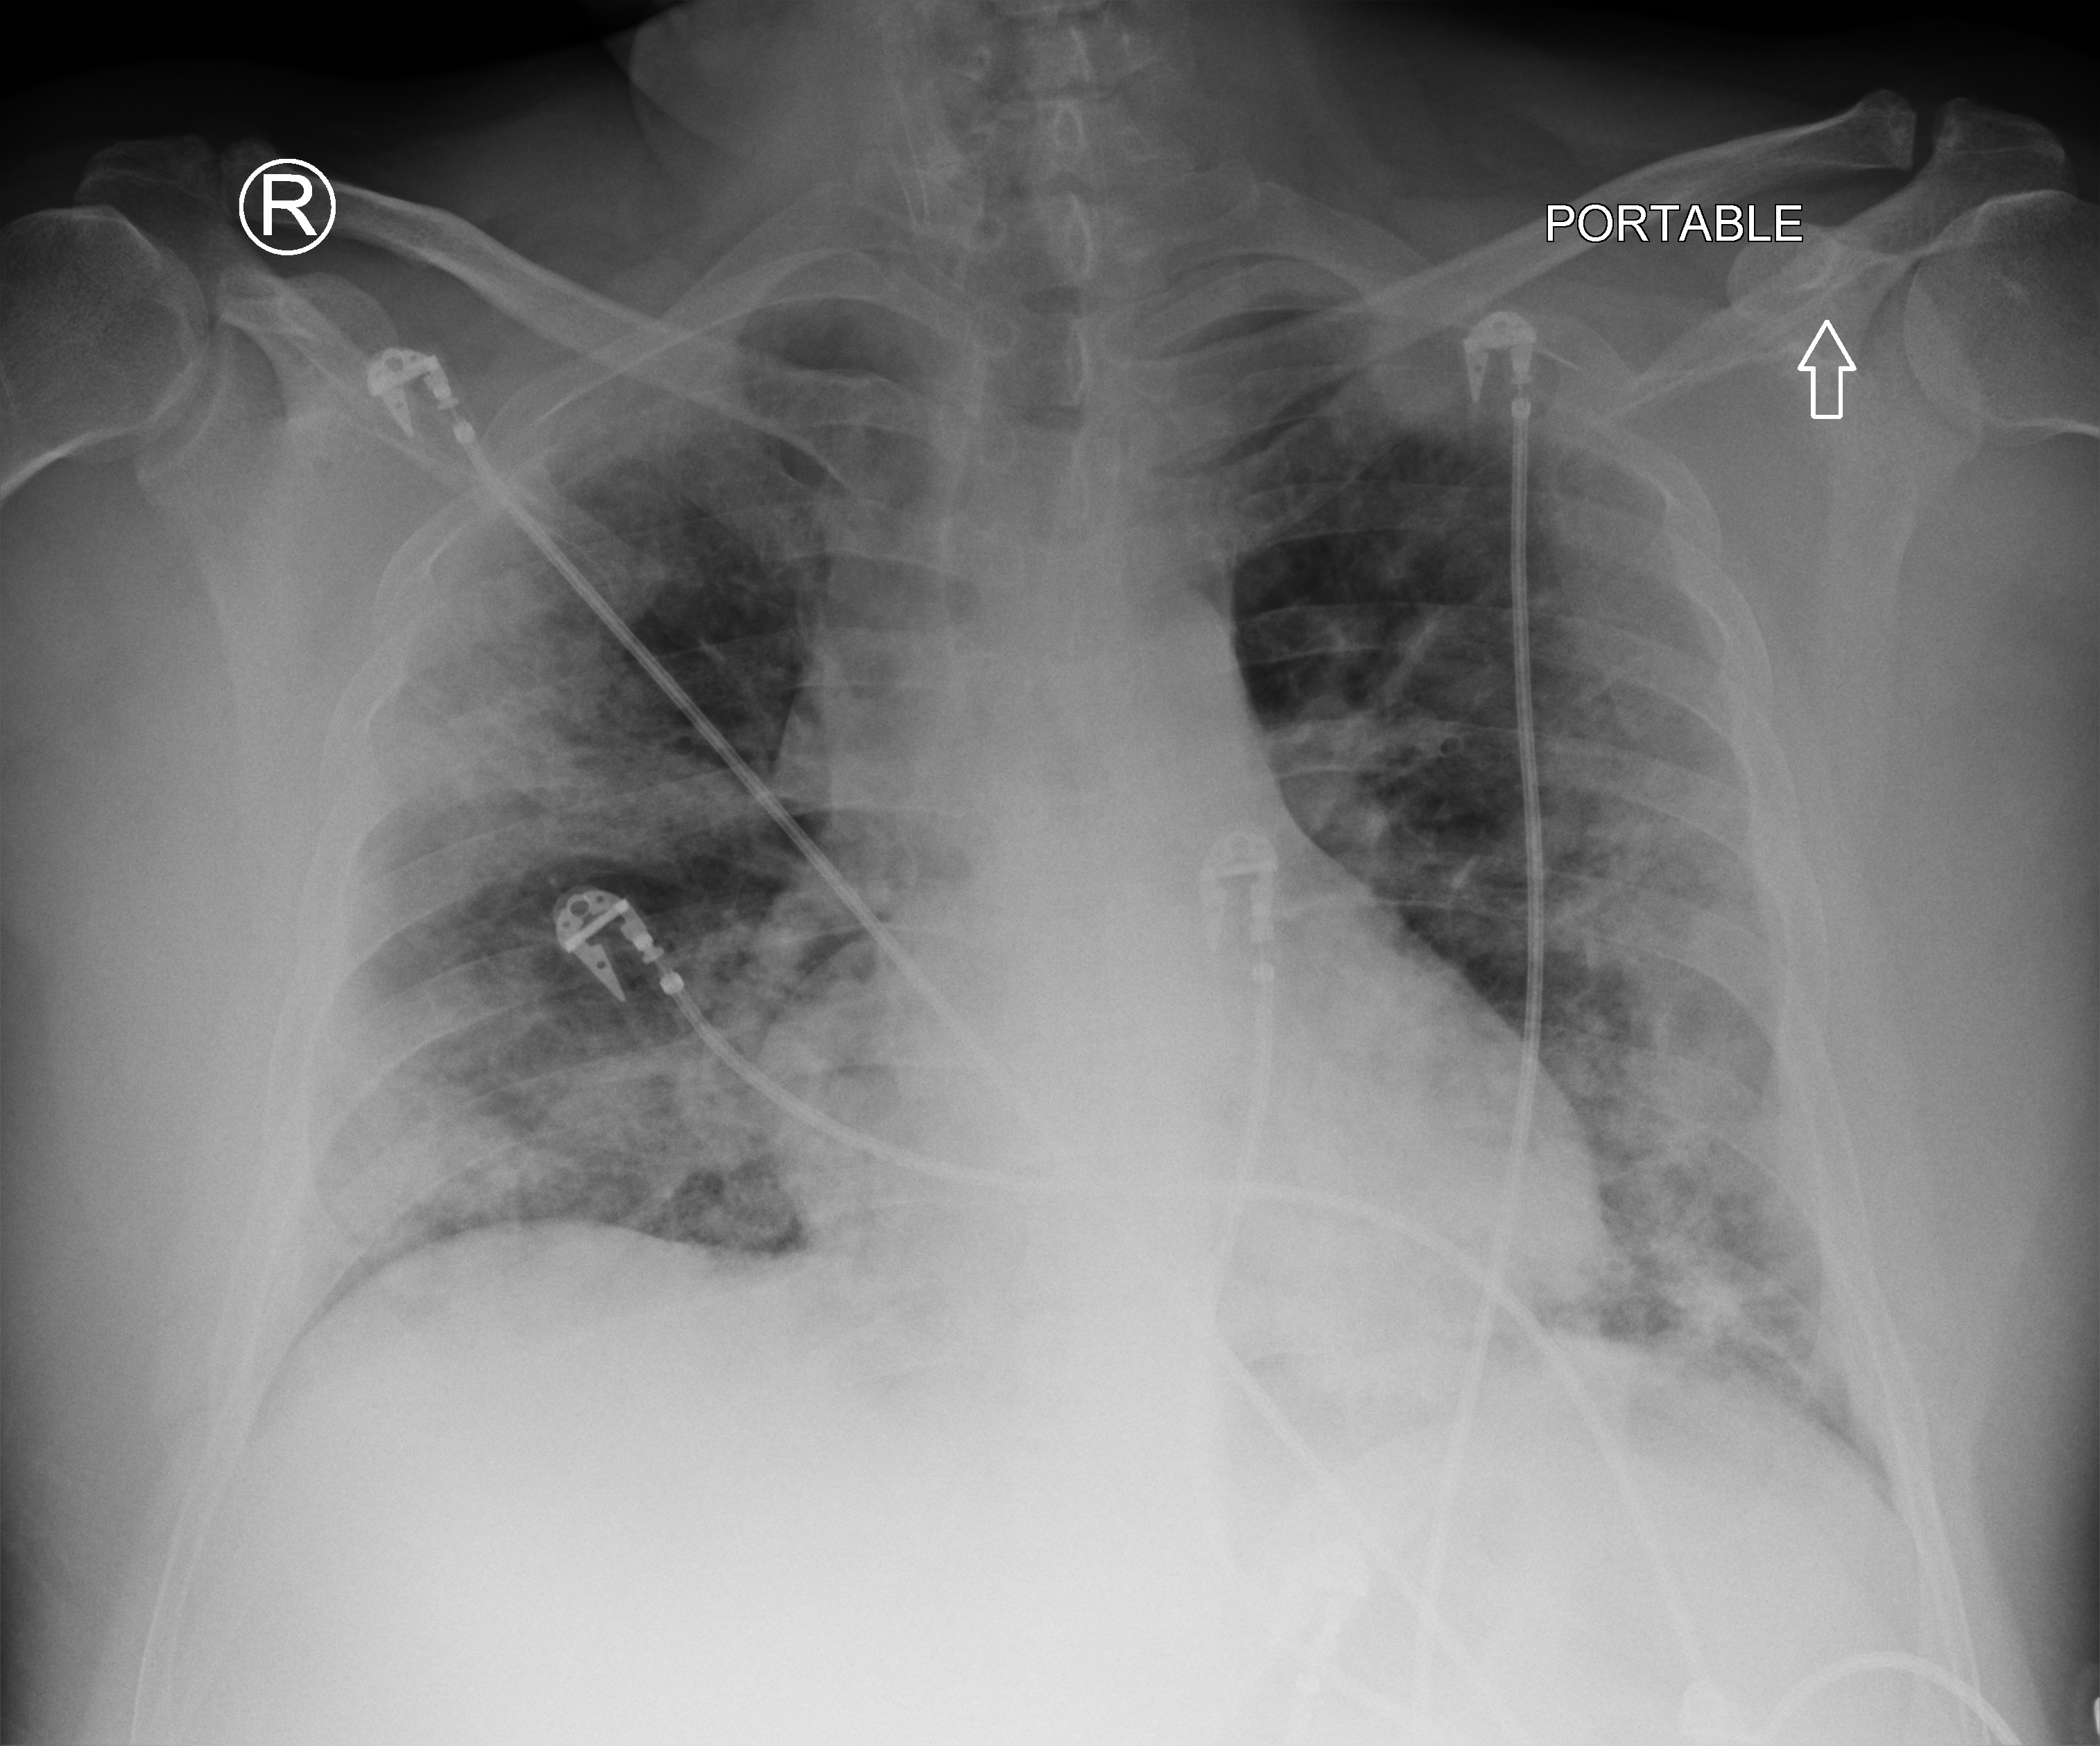
Portable chest radiograph. Adult patient hospitalised with COVID-19, age 18–59 years.
Admission-level facts for this patient (not findings on this image; timing relative to this image not recorded):
- length of hospital stay: 50 days
- admitted to intensive care during this hospital stay: yes
- mechanically ventilated during this hospital stay: yes